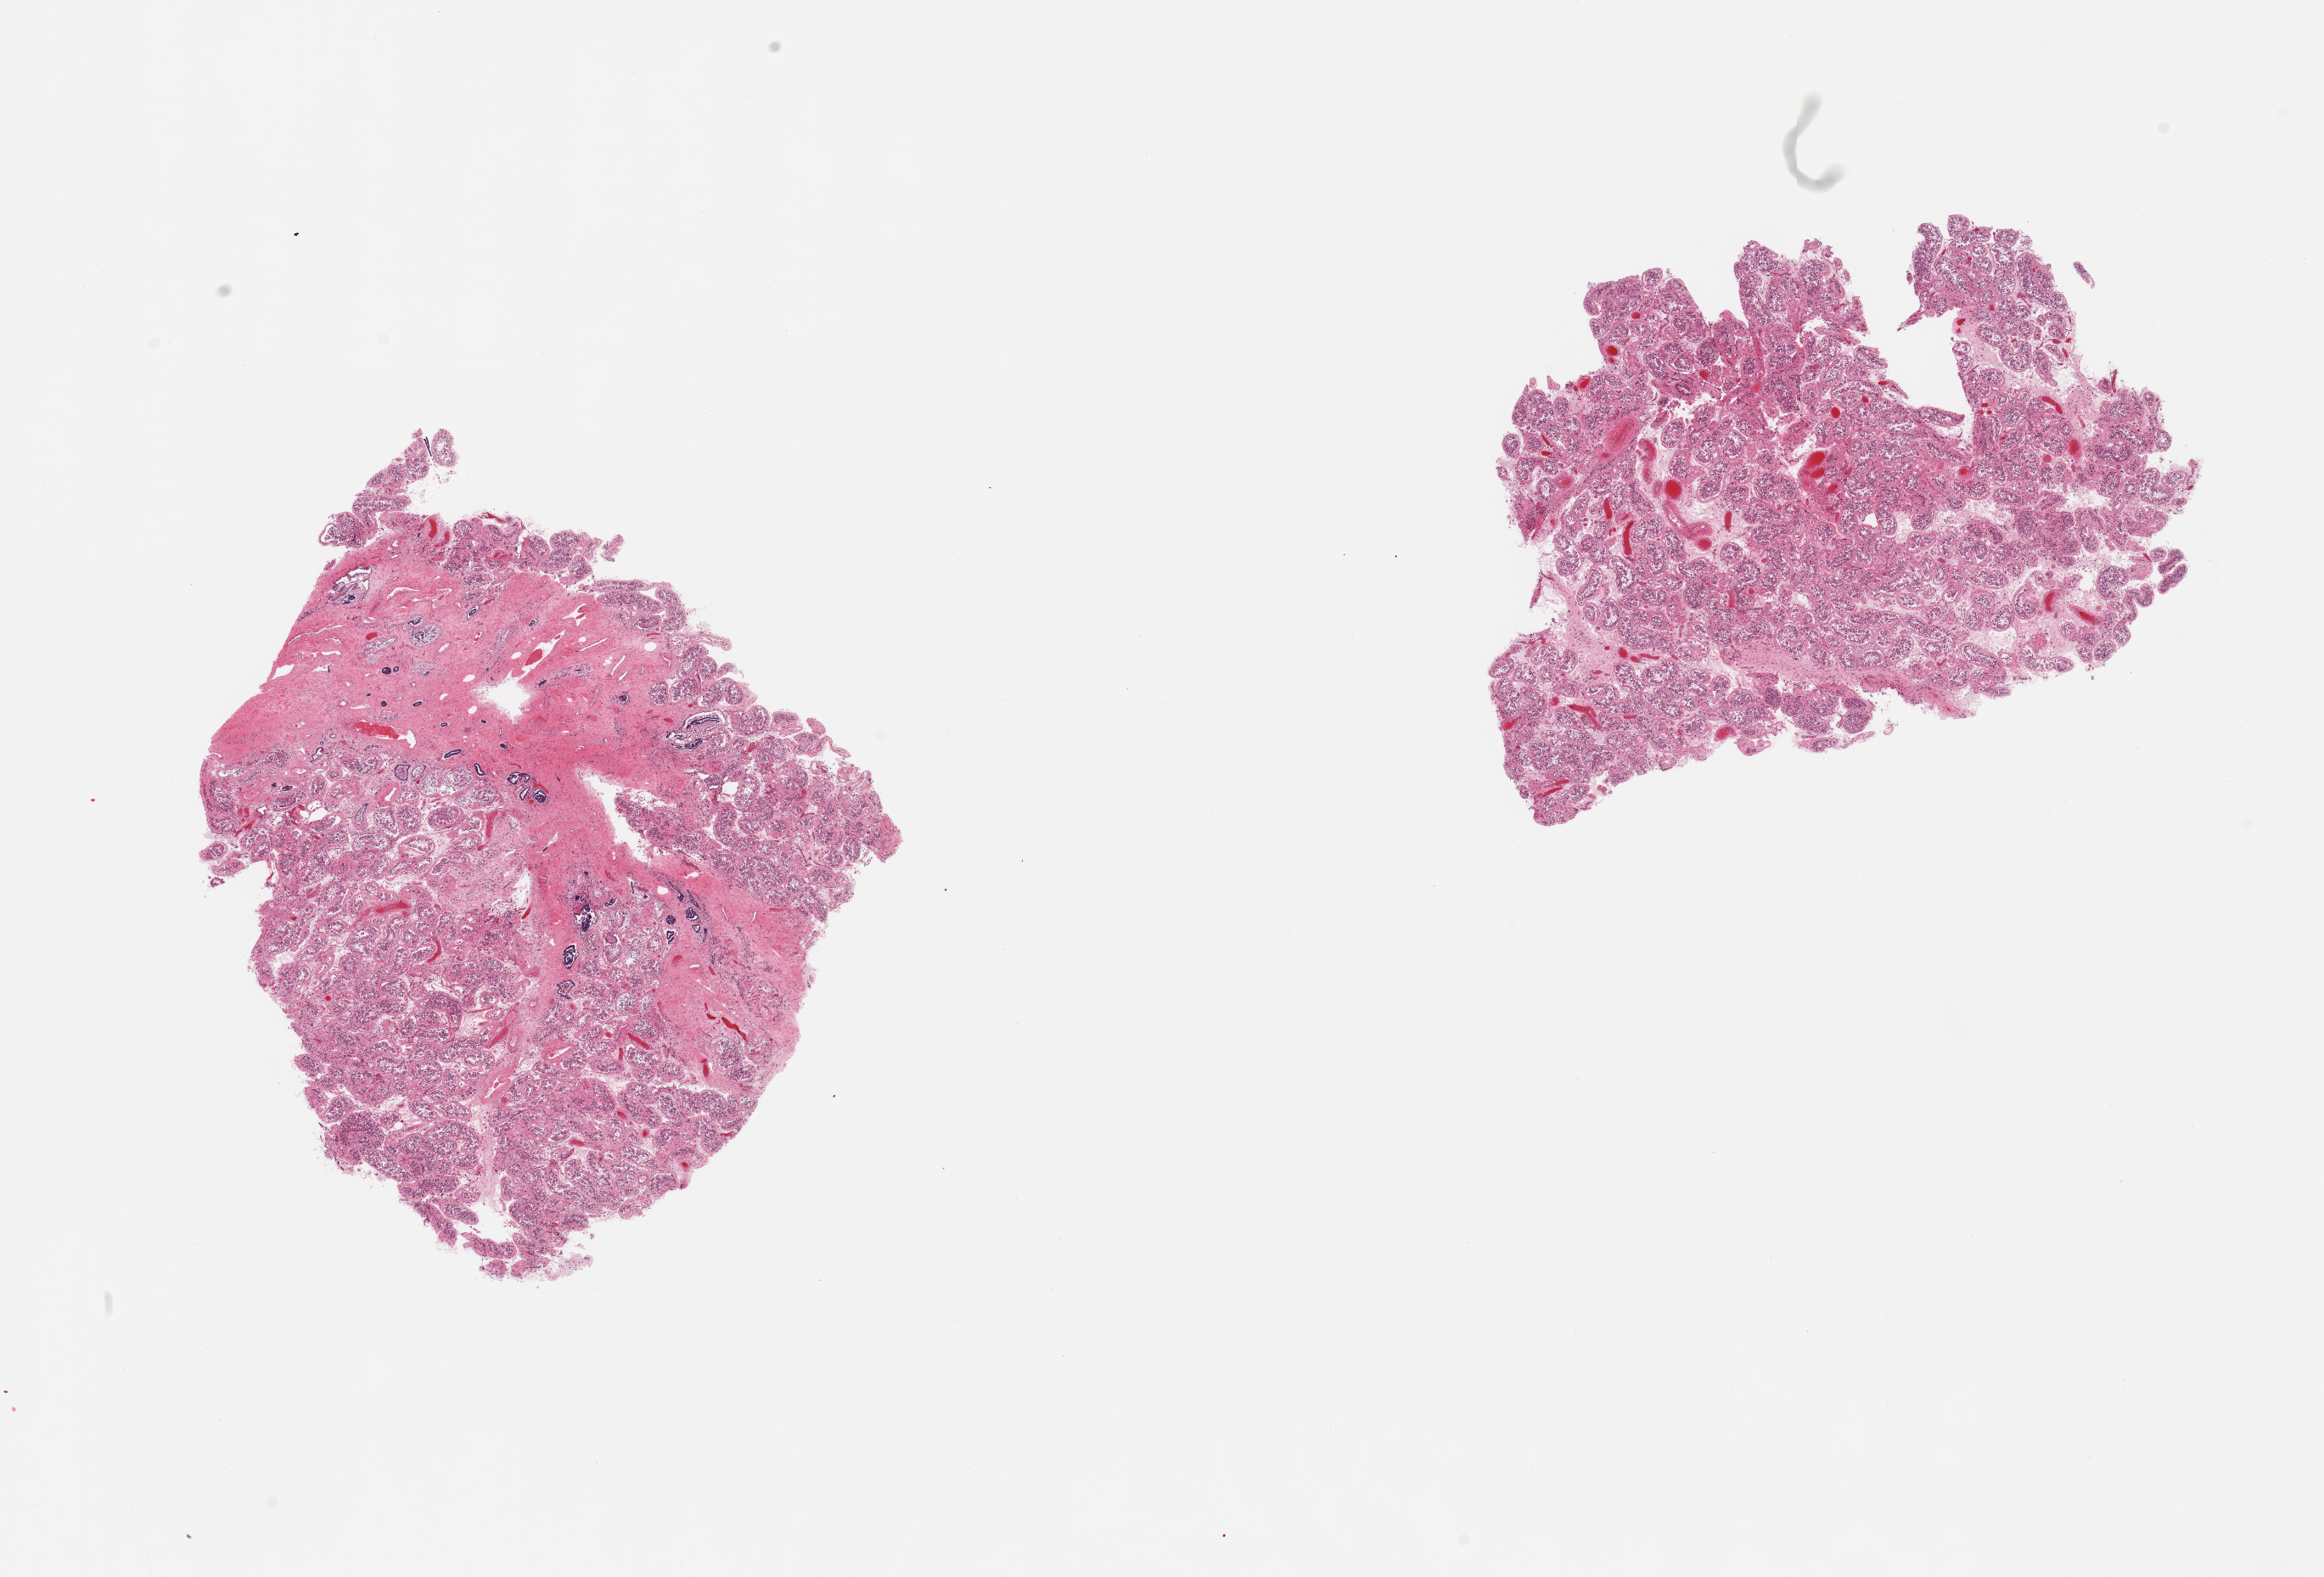
Haematoxylin and eosin whole-slide image, brightfield — shown as a low-resolution overview of the whole scanned area (about 21.7 x 14.7 mm, slide scanned at 20x). PAXgene-fixed, paraffin-embedded tissue. Target tissue: testis. Tissue donor sample. Male donor.
Reviewer comment on this tissue sample: 2 pieces; arrested spermatogenesis; focal scarring.